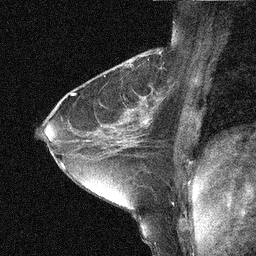
Breast MRI (dynamic contrast-enhanced), one sagittal slice. Dynamic contrast-enhanced study with each time point stored as its own series, time point 2 of 3 at this slice position (early post-contrast, ordered by acquisition time). 1.5 T. TE 5 ms, TR 10.3 ms. 3 mm slice thickness. 256 × 256 image matrix, field of view 180 × 180 mm. Patient: female, 31 years. From the clinical record (not read from this slice): setting: breast cancer imaged before/during neoadjuvant chemotherapy; receptor status: HER2-positive.
Outlined on this slice (semi-automatic segmentation, software-assisted and operator-edited):
- analysis volume of interest (the breast-tissue region the enhancement analysis was run in; not a lesion): bounding box [x1, y1, x2, y2] px = [136, 131, 181, 168]
- tumour enhancement mask (voxels above the 90 % enhancement threshold inside the analysis volume of interest): [140, 139, 142, 141]